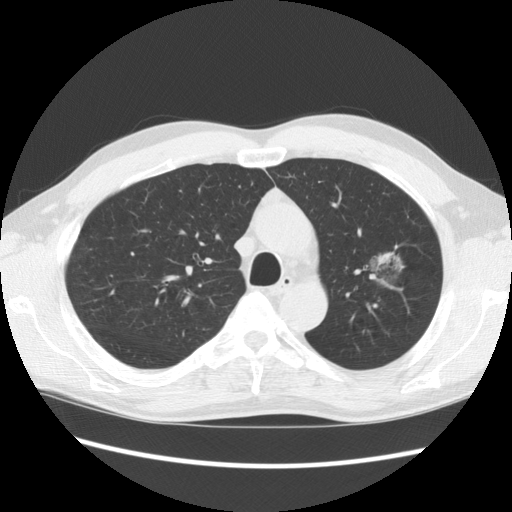
Low-dose screening chest CT, axial slice. Second screening round (one year after baseline). Lung window (W 1500 / L -600 HU). Slice 98 of 139 in the series. 512 × 512 image matrix, field of view 360 × 360 mm. Male participant, aged 61 years at enrolment.
Lesion marked by an expert reader, box from (x=348, y=225) to (x=422, y=298) px. The exam's reader record, not a measurement of the box and not confirmed to be the same lesion: non-calcified nodule or mass ≥4 mm, left upper lobe, 34 × 32 mm, poorly defined margins, mixed attenuation, pre-existing on the prior screen: yes; interval growth: no. Participant outcome: lung cancer diagnosed 704 days after this screen (after the third annual screen) — bronchiolo-alveolar adenocarcinoma, NOS, left upper lobe, well differentiated (G1), stage IB (AJCC 6th edition), 44 mm at pathology.